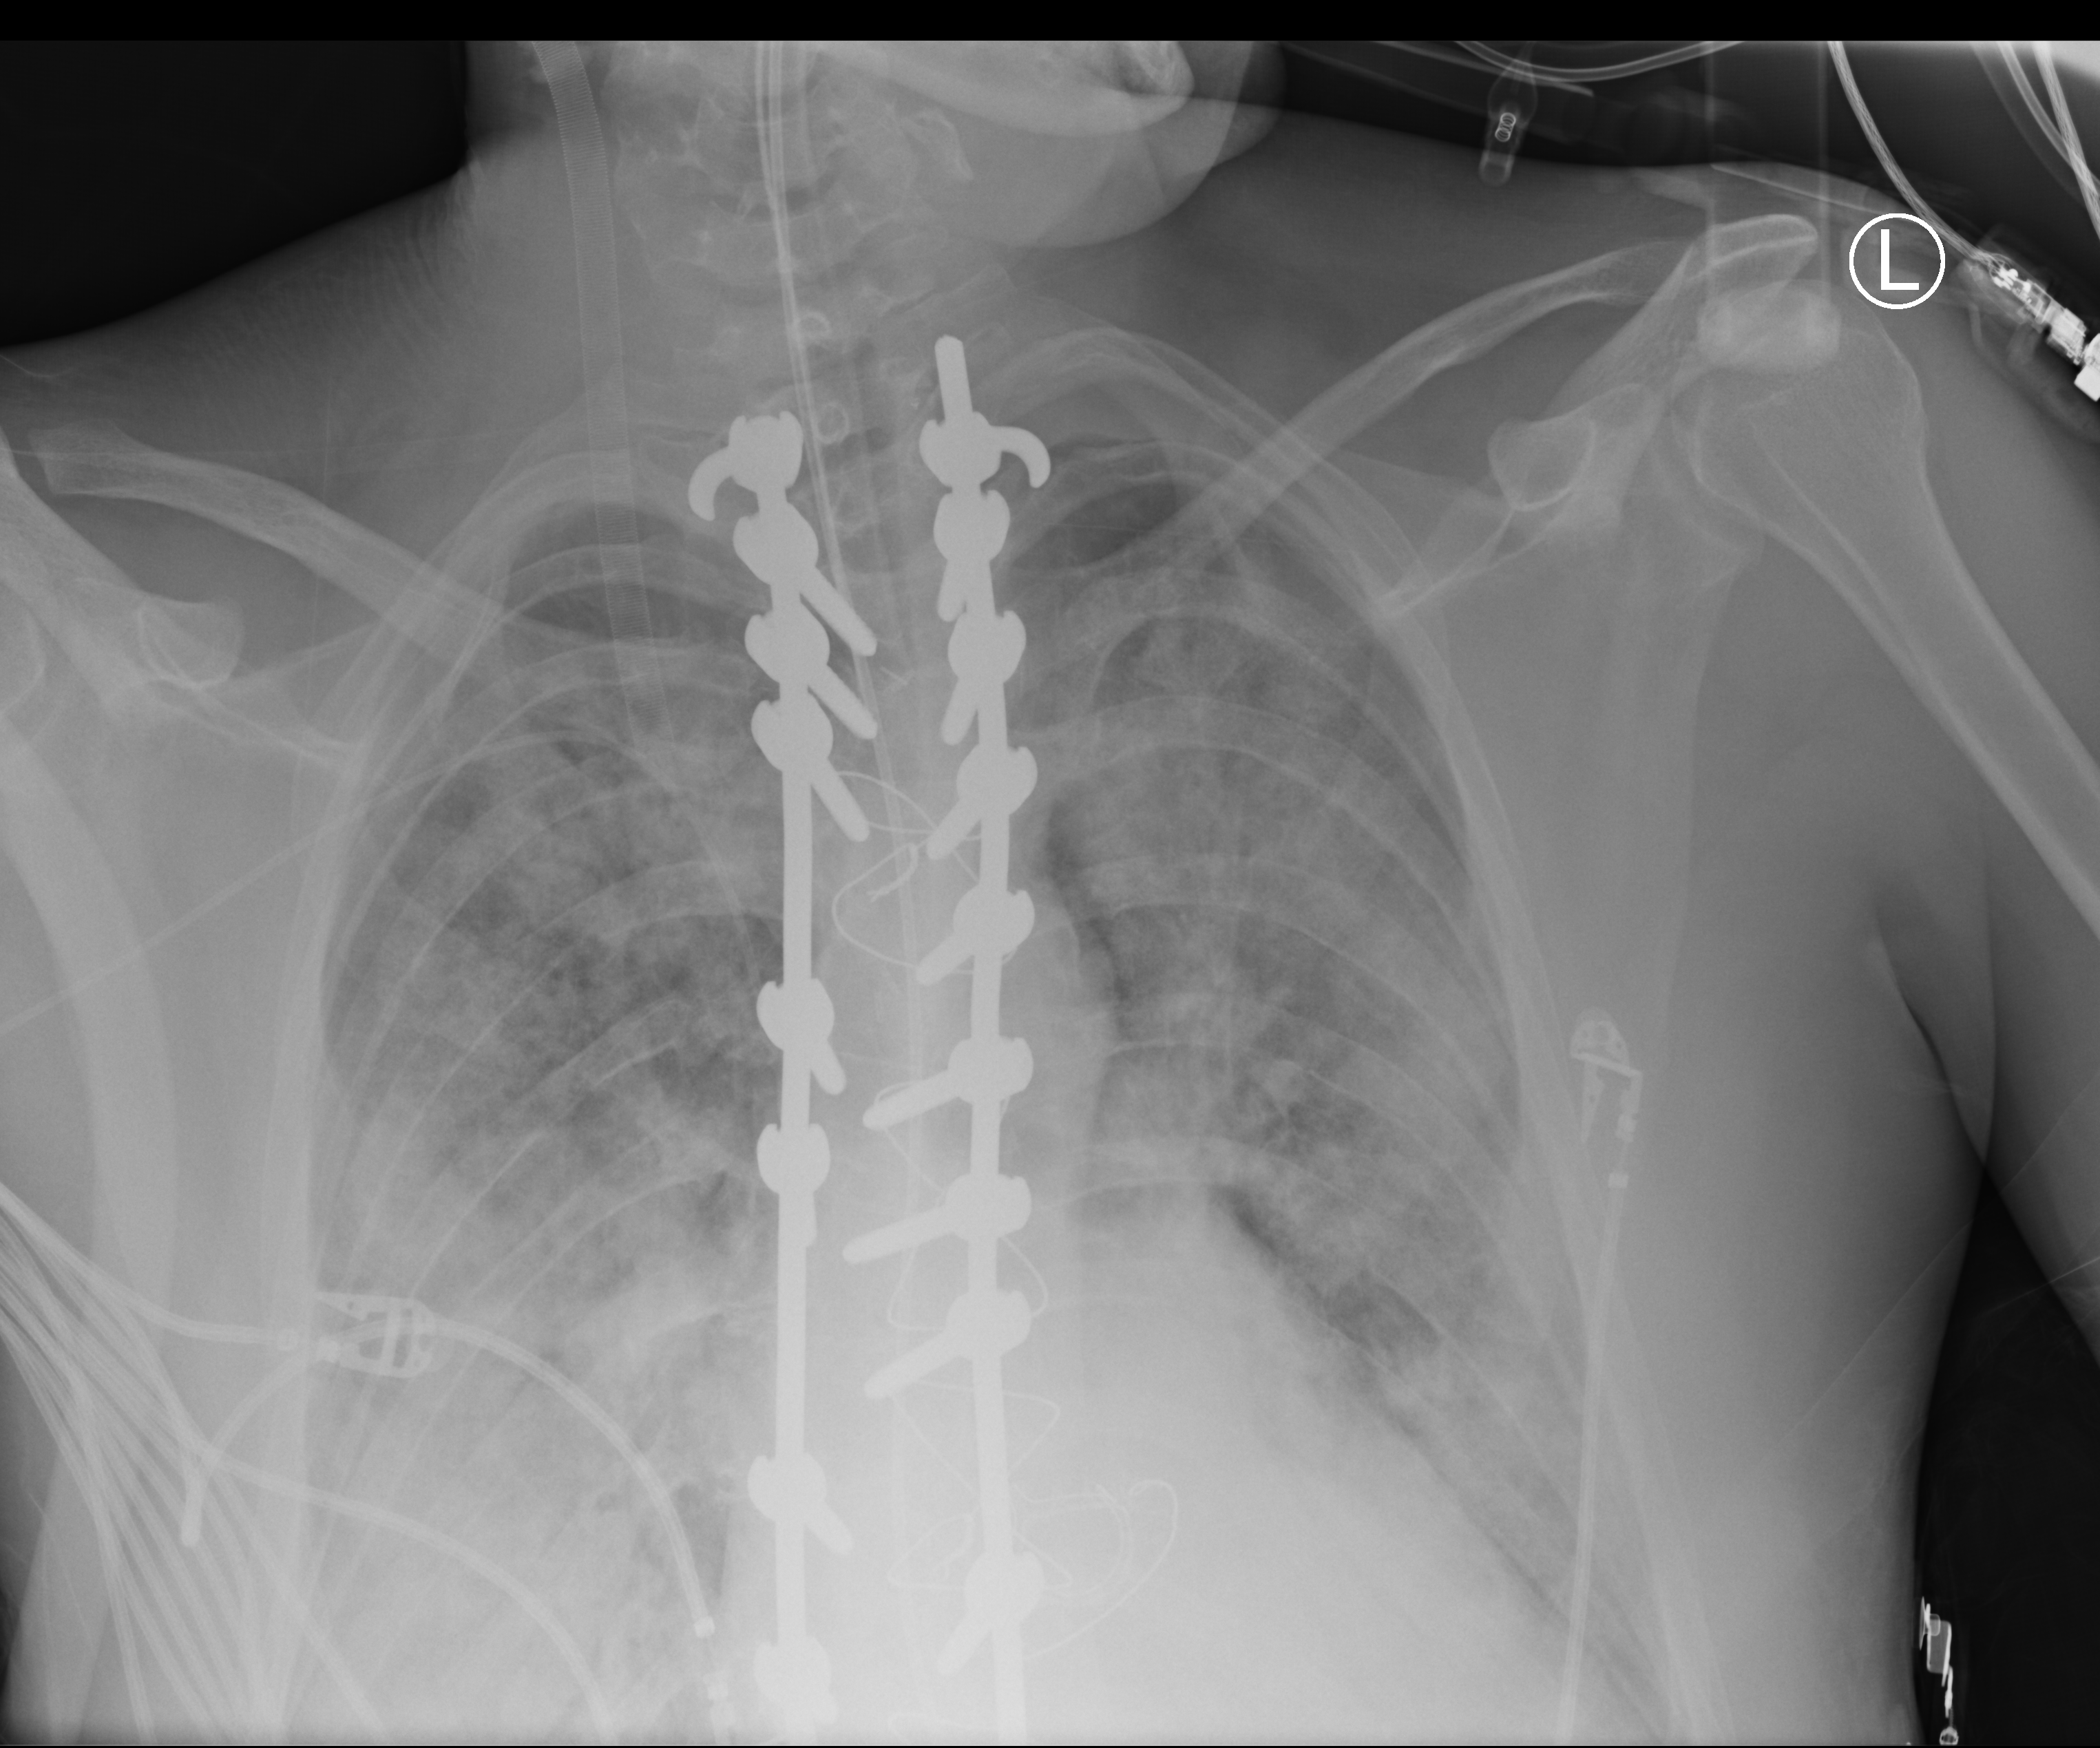
Chest X-ray; anteroposterior (AP) projection. Adult patient hospitalised with COVID-19, age 18–59 years.
Admission-level facts for this patient (not findings on this image; timing relative to this image not recorded): admitted to intensive care during this hospital stay: yes; mechanically ventilated during this hospital stay: yes; COPD (admission record): no.